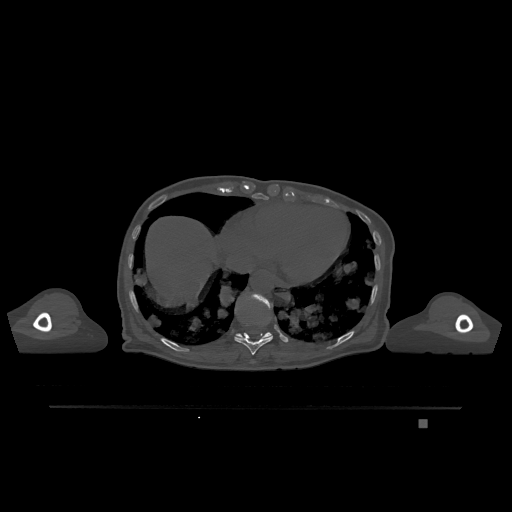
CT including the spine, one axial slice. Slice 626 of 1317 in the series (ordered by position). Bone window (W 1800 / L 400 HU). 0.5 mm slice thickness. 512 × 512 image matrix. Female patient, age 74 years. Case-level facts recorded for this patient, not image findings: primary cancer: lung; vertebrae with lytic lesions (as recorded): T1, T4, T5, T6, L4, L5.
Annotated regions visible in this slice (semi-automatic segmentation, software-assisted and operator-edited):
- T10 vertebra: bounding box [x1, y1, x2, y2] px = [234, 322, 273, 355]
- T11 vertebra: [236, 293, 273, 338]